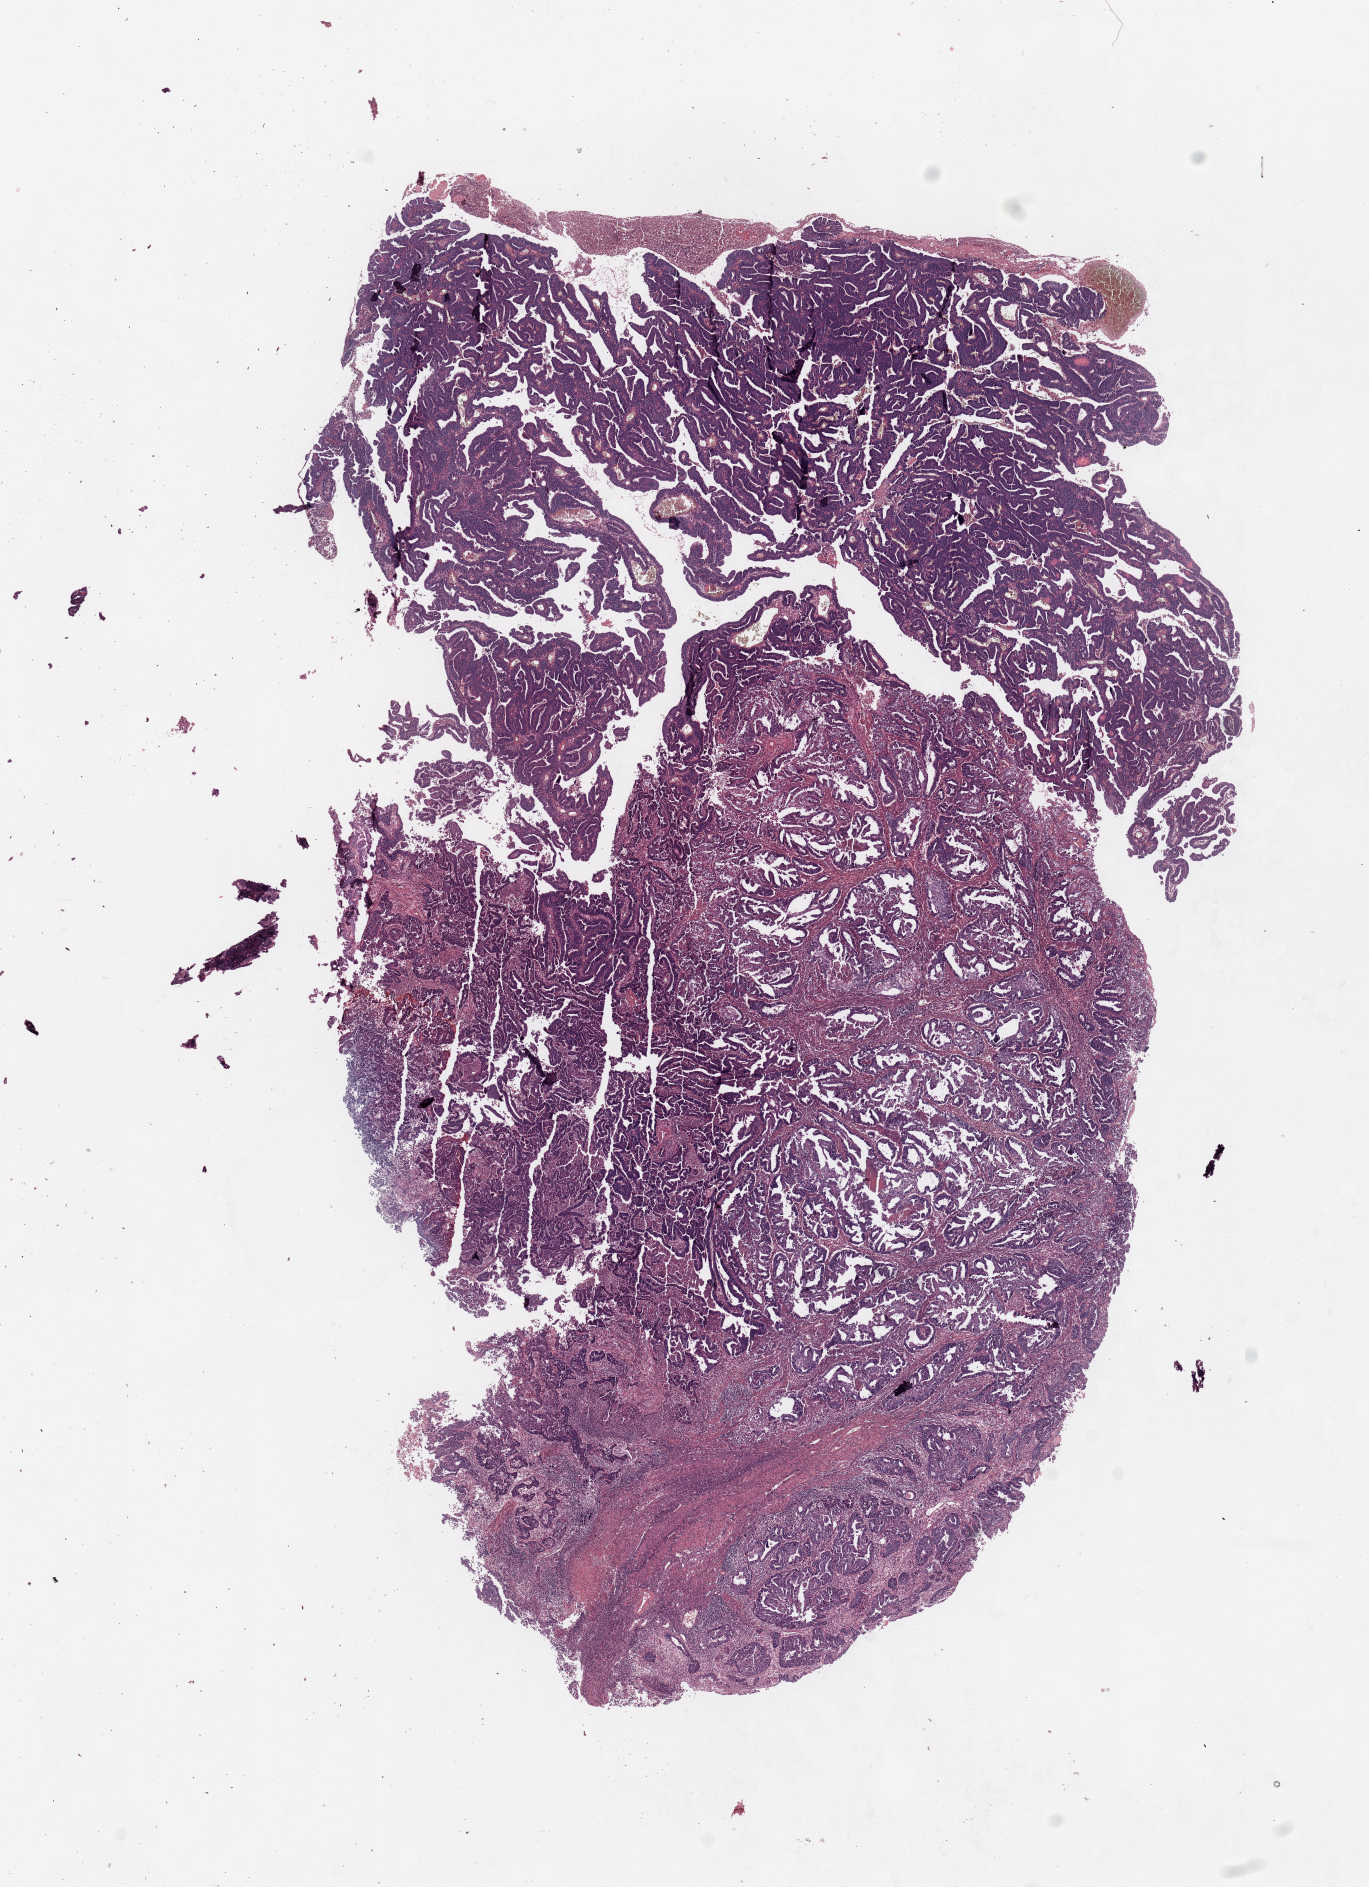
Digitized H&E tissue section (whole slide) — a low-resolution overview of the entire scanned area, about 10.8 x 14.9 mm (from a 20x scan); tumour tissue sample, uterus. Patient: female, age 55 years. Histologic grade: G3 (poorly differentiated).
- histologic diagnosis: Endometrioid adenocarcinoma, NOS
- AJCC pathologic stage: I